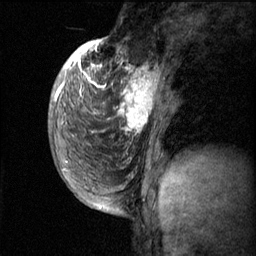
Breast MRI (dynamic contrast-enhanced), one sagittal slice; dynamic contrast-enhanced series, image 2 of 3 at this slice position (ordered by acquisition); 1.5 T; TE 4.2 ms, TR 11.1 ms; 2 mm slice thickness; 256 × 256 image matrix, field of view 180 × 180 mm. Patient: female, 50 years.
Structures marked on this image (semi-automatically segmented with operator editing):
- analysis volume of interest (the breast-tissue region the enhancement analysis was run in; not a lesion): box from (x=82, y=56) to (x=168, y=143) px
- tumour enhancement mask (voxels above the 70 % enhancement threshold inside the analysis volume of interest): (x=82, y=56)–(x=160, y=133)